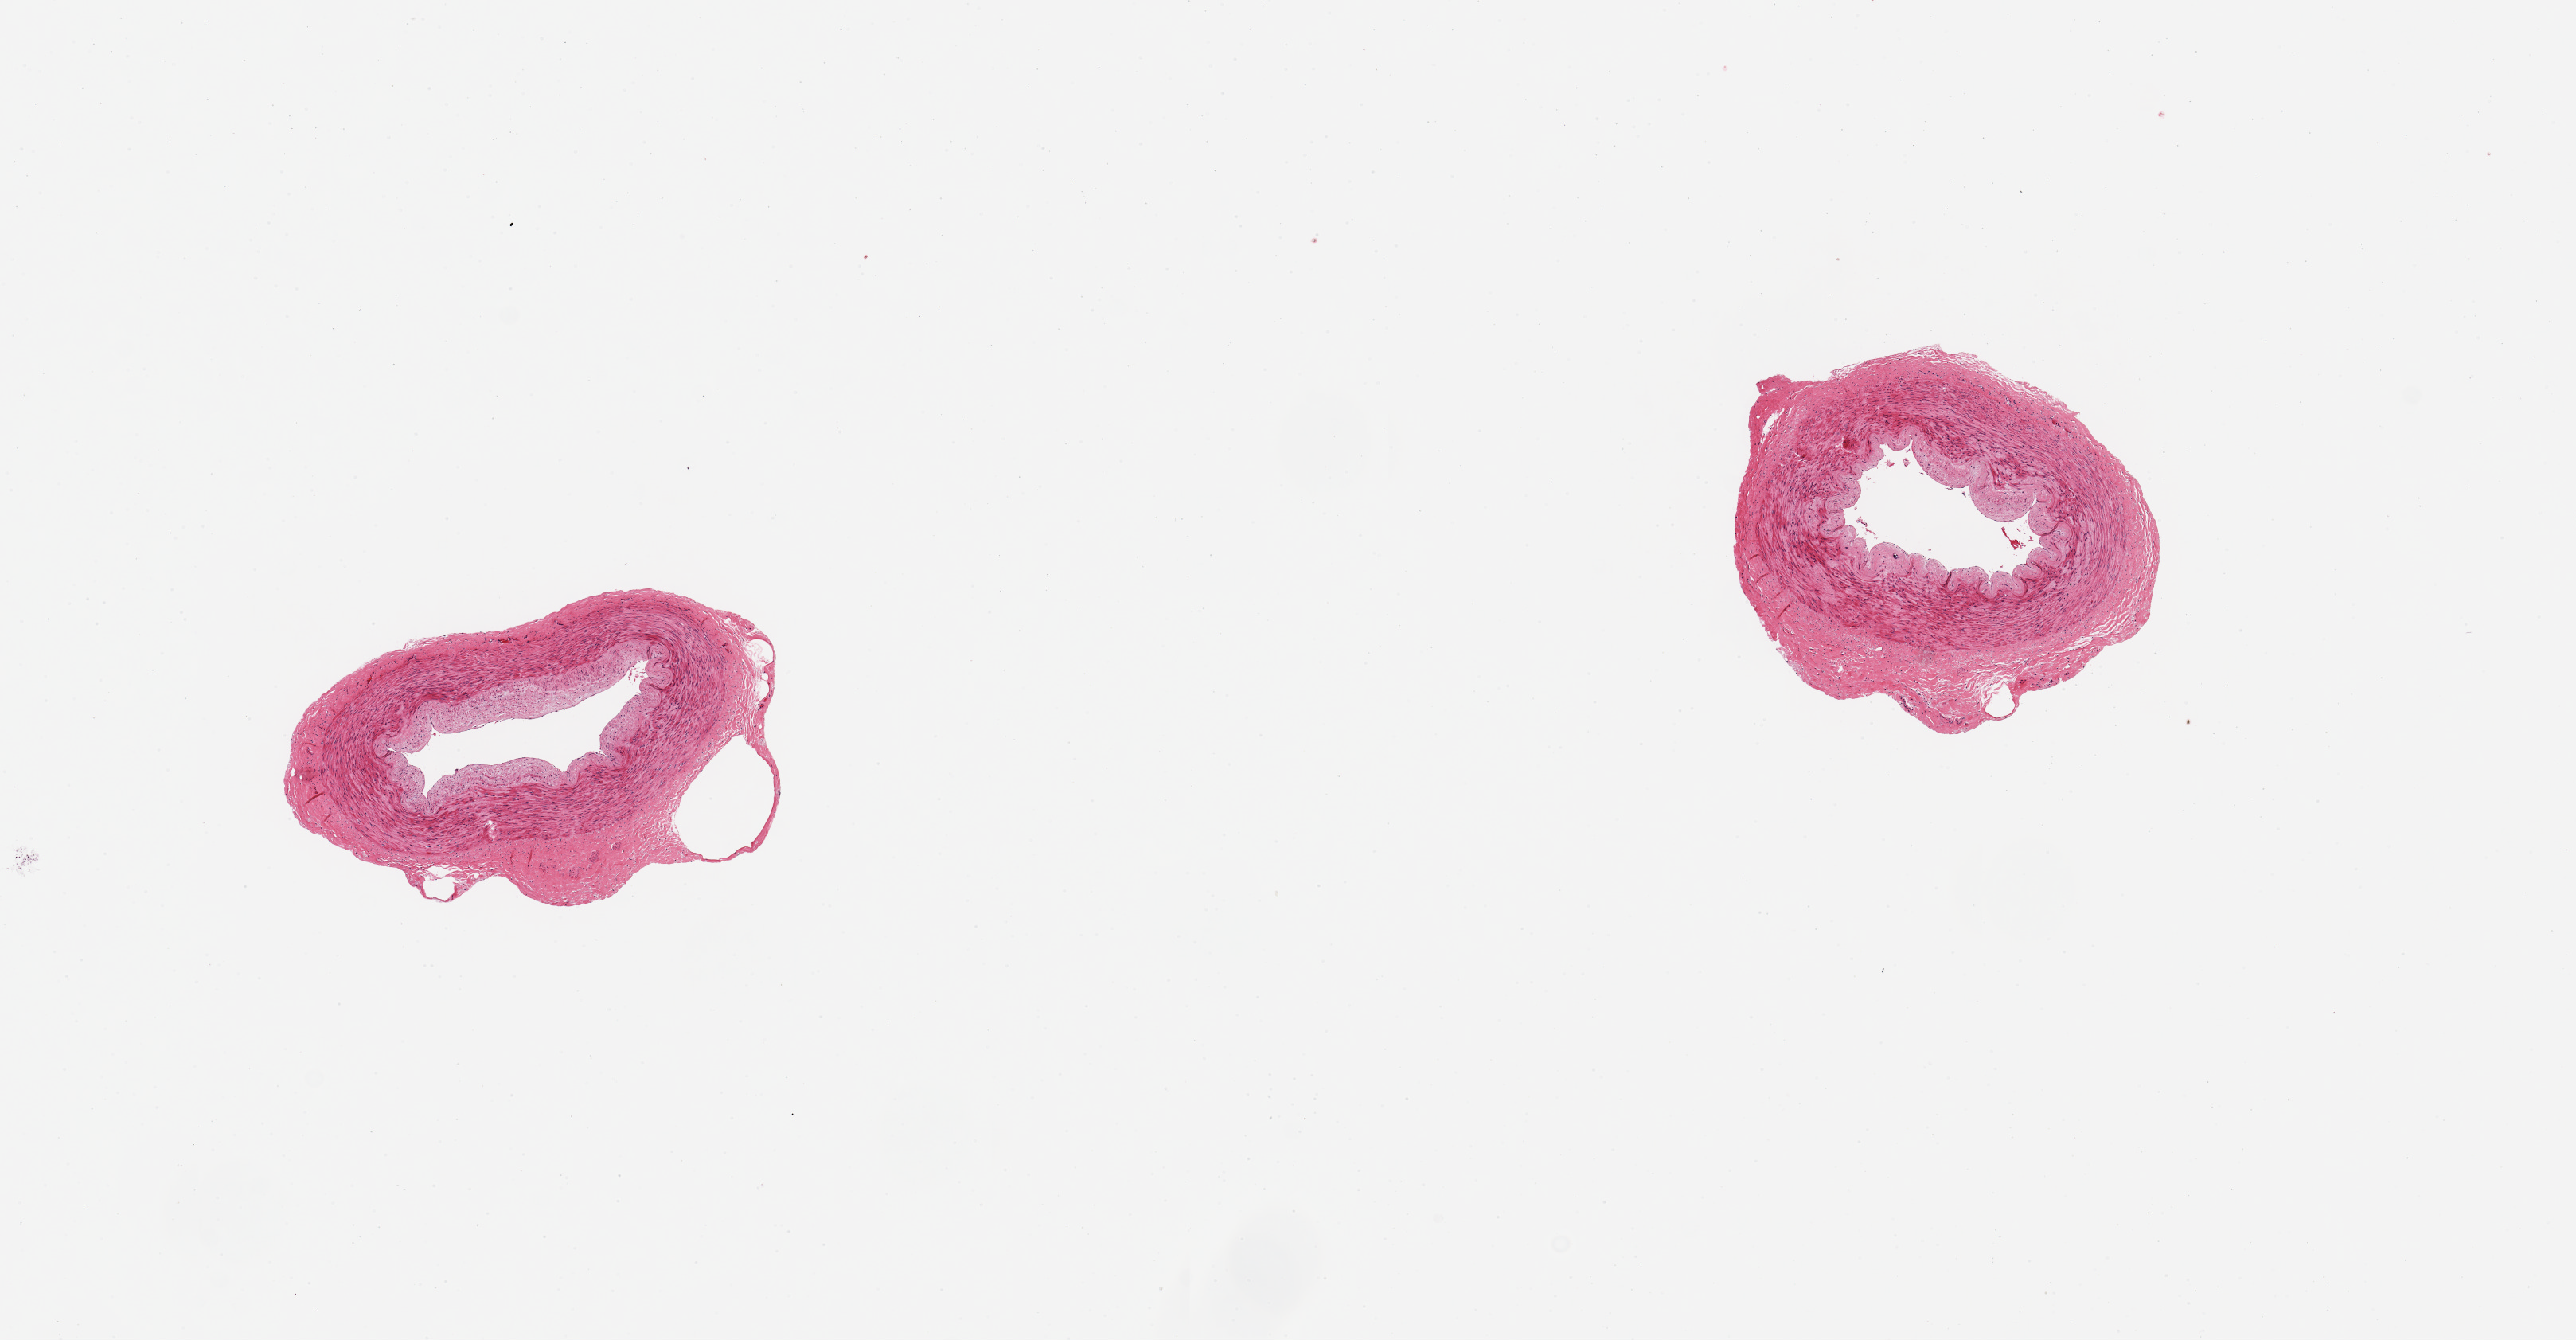
Digitized haematoxylin and eosin-stained section — whole scanned area (about 12.8 x 6.7 mm, from a 20x scan) shown as a low-resolution overview. PAXgene-fixed, paraffin-embedded tissue. Section of tibial artery (target tissue). Tissue donor sample.
Review note (as recorded): 2 pieces, ~2mm d.